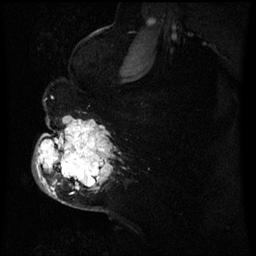
Breast MRI (dynamic contrast-enhanced), one sagittal slice. Slice 44 of 60 in the series (ordered by position). Dynamic contrast-enhanced series, image 2 of 3 at this slice position (ordered by acquisition). 1.5 T. TE 4.2 ms, TR 8 ms. 2.5 mm slice thickness. 256 × 256 image matrix. Female patient, age 50 years.
Structures marked on this image (semi-automatically segmented with operator editing):
- analysis volume of interest (the breast-tissue region the enhancement analysis was run in; not a lesion): bounding box (x1, y1, x2, y2) in pixels: (38, 120, 112, 199)
- tumour enhancement mask (voxels above the 70 % enhancement threshold inside the analysis volume of interest): (40, 126, 107, 191)